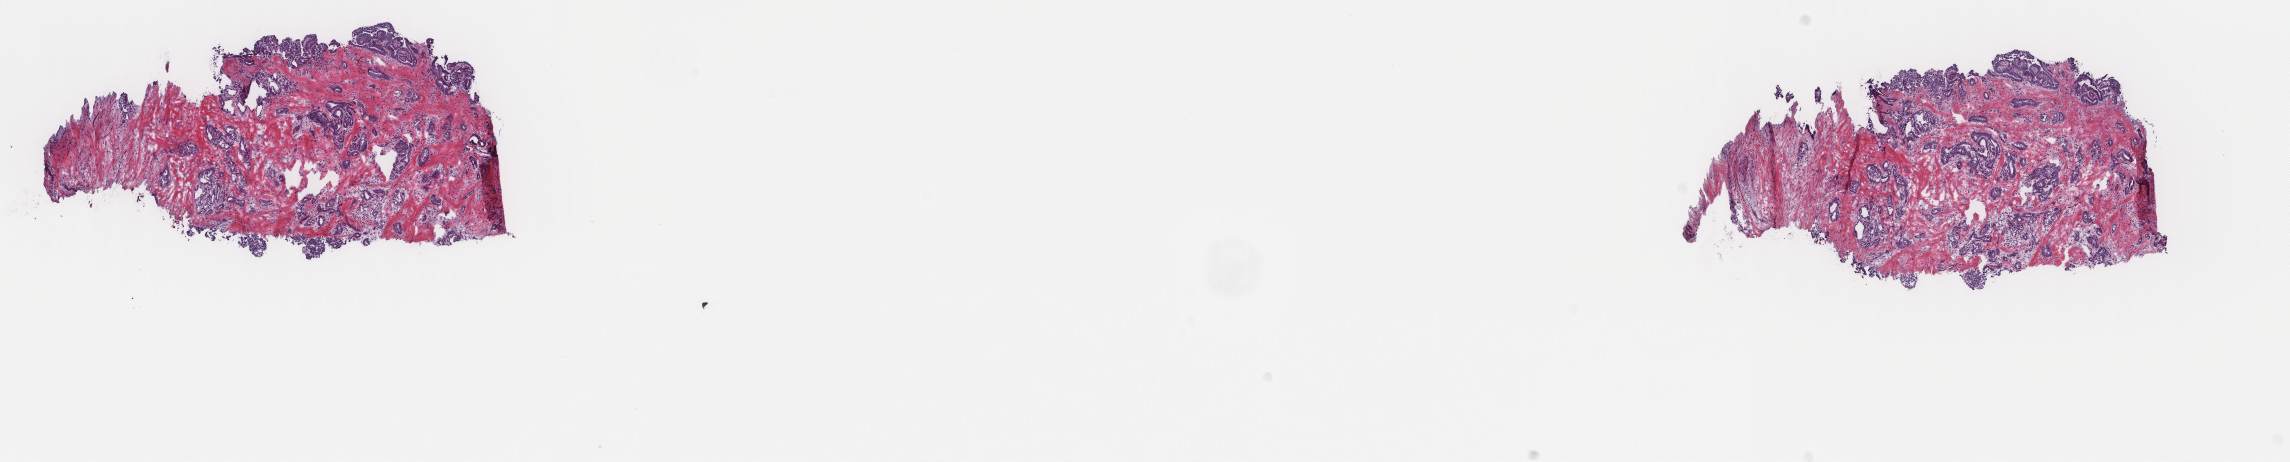
Digitized H&E tissue section (whole slide) — shown as a low-resolution overview of the whole scanned area (about 18.2 x 3.7 mm). Frozen section. Sample: primary tumour, thyroid. Female, age 61 years at initial diagnosis. Slide review estimates, as recorded: tumour cells 85%, tumour nuclei 75%, normal cells 0%, stromal cells 15%, necrosis 0%. Inflammatory infiltration, as recorded: lymphocyte infiltration 0%, monocyte infiltration 0%, neutrophil infiltration 0%.
* laterality: right
* AJCC pathologic stage: III (7th edition)
* diagnosis: Papillary adenocarcinoma, NOS